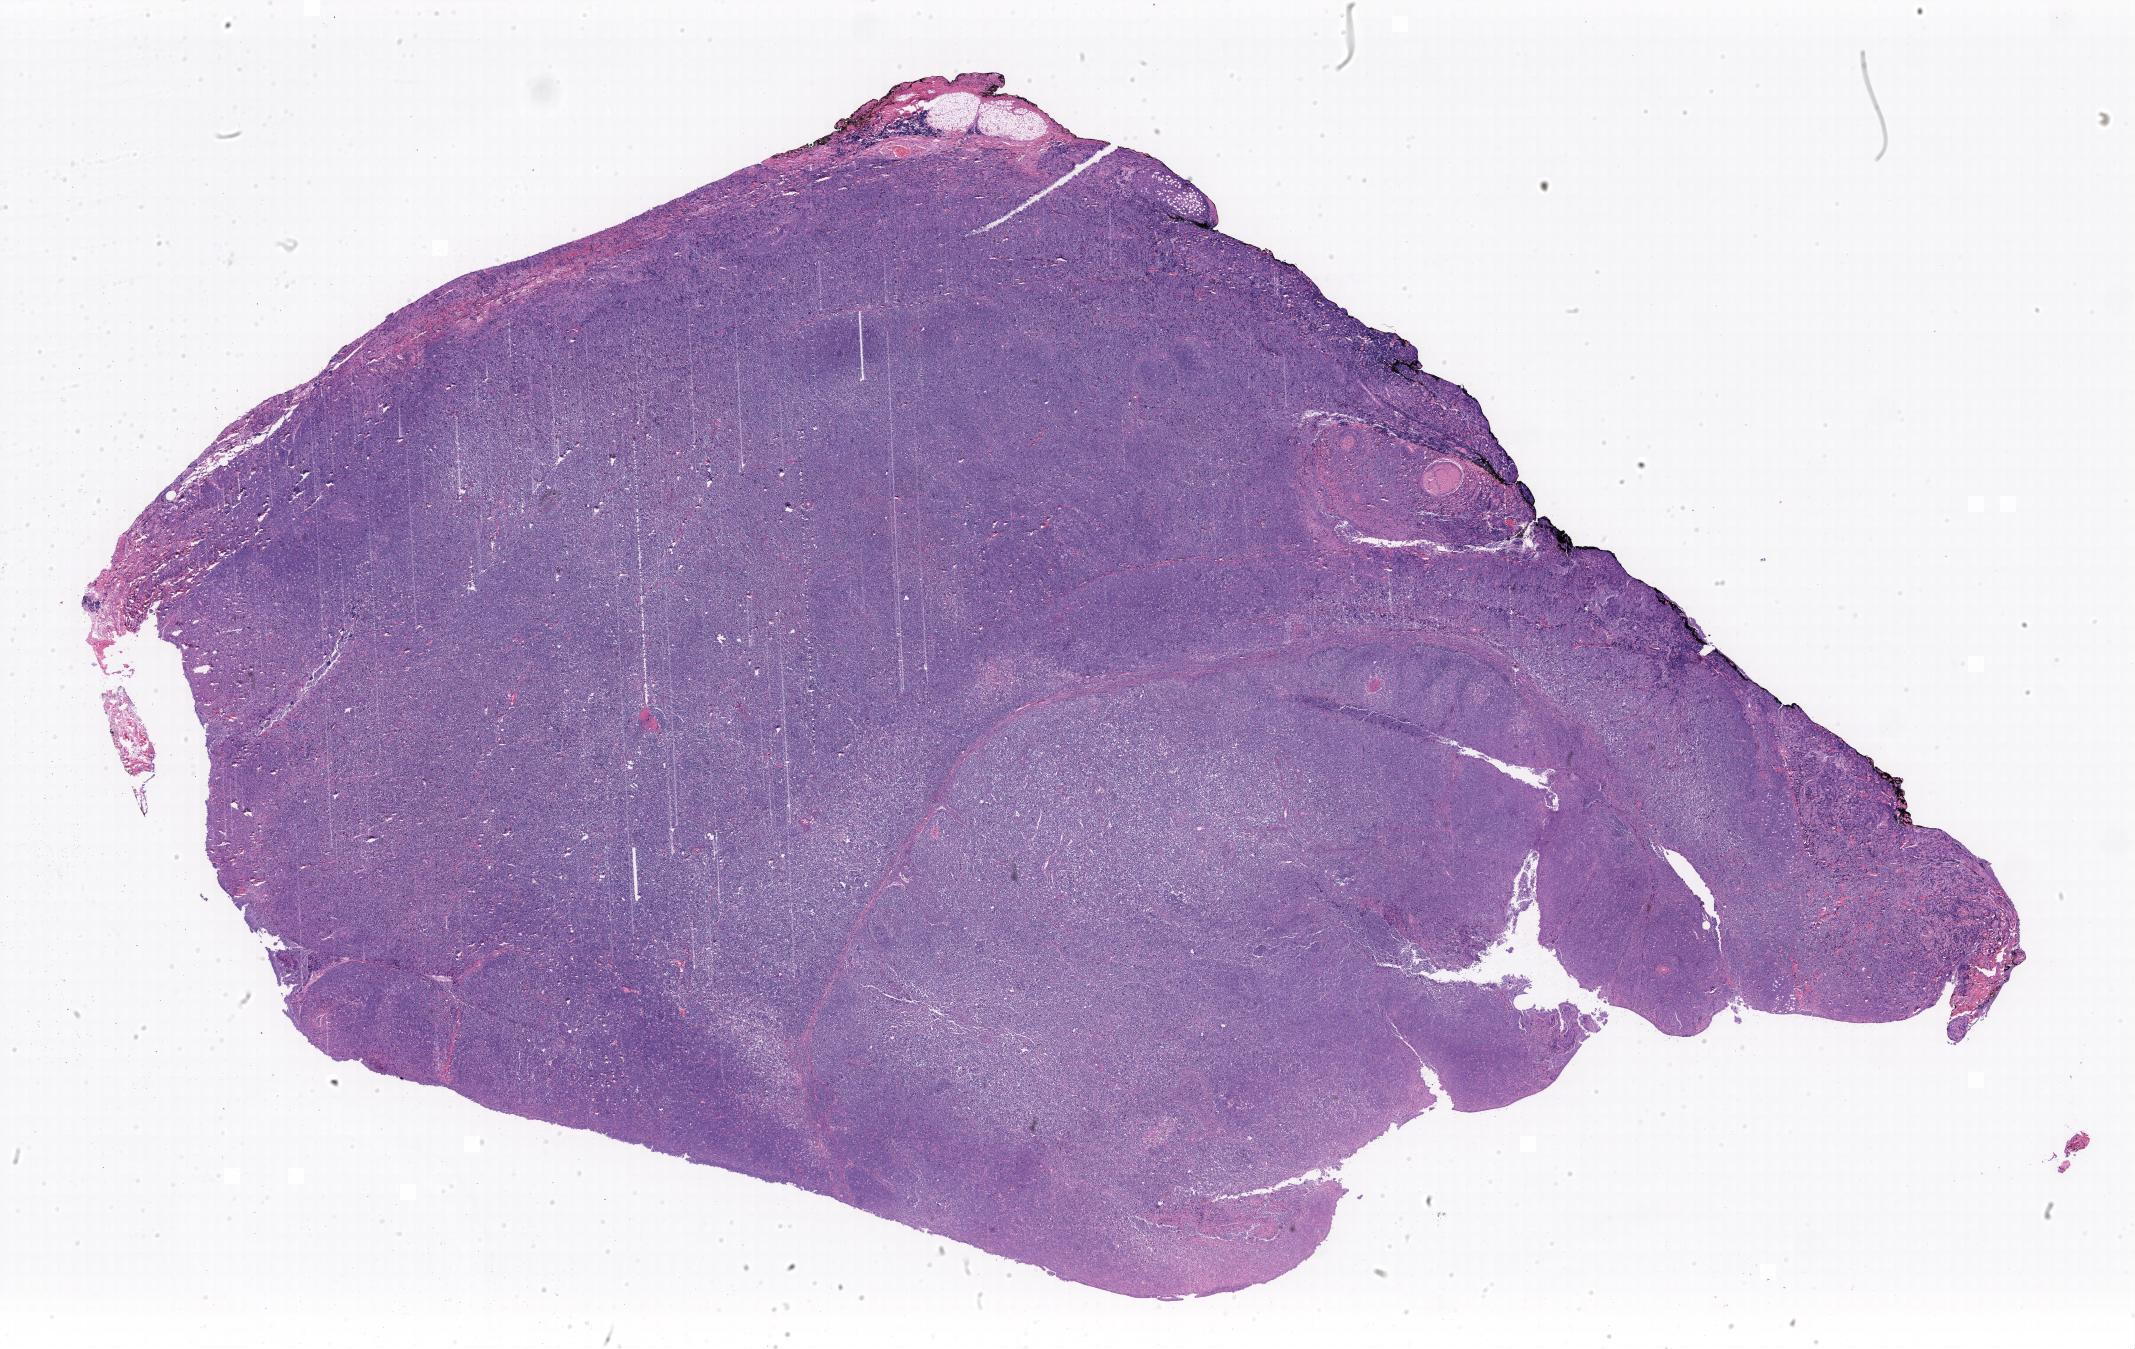
Digitized hematoxylin and eosin (H&E)-stained section — shown as a low-resolution overview of the whole scanned area, specimen: tumor tissue, anatomic site: lymph node of head and neck. Male, age 6 years at initial diagnosis.
Diagnosis: Burkitt lymphoma, NOS.